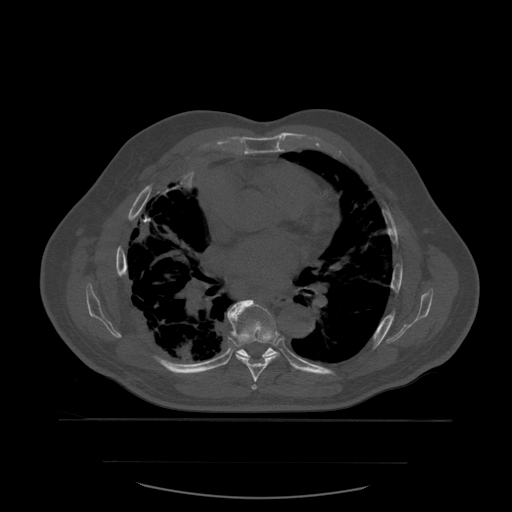
CT including the spine, one axial slice. Slice 377 of 590 in the series (ordered by position). Bone window (W 1800 / L 400 HU). 512 × 512 image matrix, field of view 479 × 479 mm. Patient age 71 years. Case-level facts recorded for this patient, not image findings: primary cancer: lung; vertebrae with lytic lesions (as recorded): T1, T2, L5, S1.
Annotated regions visible in this slice (semi-automatically segmented with operator editing):
- T6 vertebra: box from (x=252, y=385) to (x=257, y=390) px
- T7 vertebra: (x=228, y=299)–(x=280, y=383)
- T8 vertebra: (x=227, y=313)–(x=280, y=360)